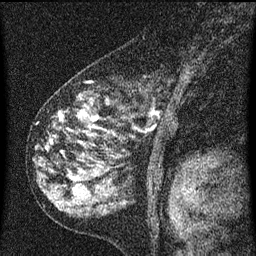
Breast MRI (dynamic contrast-enhanced), one sagittal slice; position 38 of 60 along the scan axis; dynamic contrast-enhanced series, image 2 of 3 at this slice position (ordered by acquisition); 1.5 T; TE 4.2 ms, TR 8 ms; 2 mm slice thickness; 256 × 256 image matrix. Female patient, age 55 years.
Structures marked on this image (semi-automatically segmented with operator editing):
- analysis volume of interest (the breast-tissue region the enhancement analysis was run in; not a lesion): bounding box (x1, y1, x2, y2) in pixels: (42, 72, 172, 155)
- tumour enhancement mask (voxels above the 70 % enhancement threshold inside the analysis volume of interest): (60, 112, 149, 135)